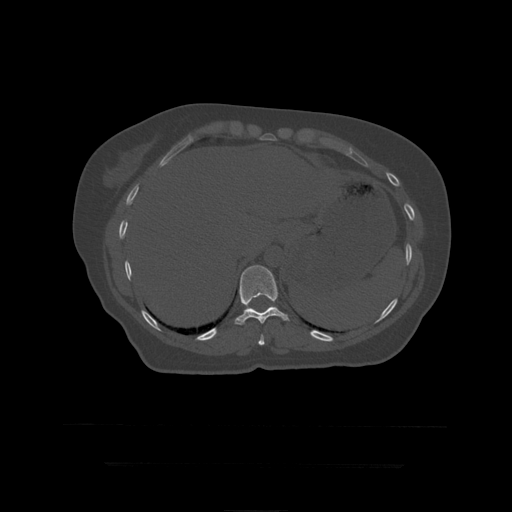
CT including the spine, one axial slice; slice 221 of 399 in the series (ordered by position); bone window (W 1800 / L 400 HU); 512 × 512 image matrix, field of view 450 × 450 mm. Patient age 41 years. From the clinical record (not read from this slice): primary cancer: breast.
Structures marked on this image (semi-automatic segmentation, software-assisted and operator-edited):
- T10 vertebra: bounding box <258,334,265,346> (left, top, right, bottom; pixels)
- T11 vertebra: <235,265,290,325>